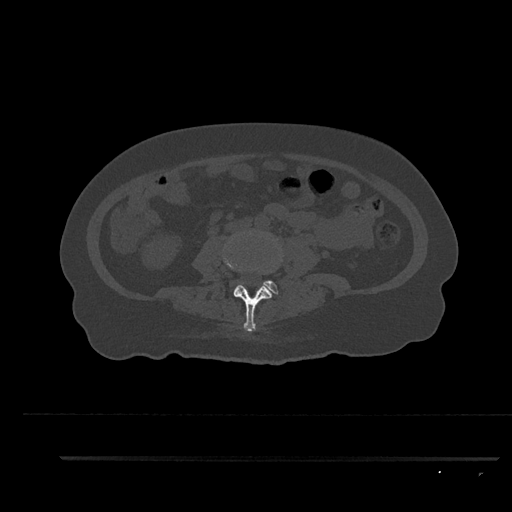
CT including the spine, one axial slice; reconstruction kernel Br40s/3; bone window (W 1800 / L 400 HU); 0.5 mm slice thickness; 512 × 512 image matrix. Patient: female, 44 years. Case-level facts recorded for this patient, not image findings: primary cancer: renal; vertebrae with lytic lesions (as recorded): L1.
Annotated regions visible in this slice (semi-automatically segmented with operator editing):
- L3 vertebra: bounding box [x1, y1, x2, y2] px = [223, 257, 277, 332]
- L4 vertebra: [263, 280, 279, 295]